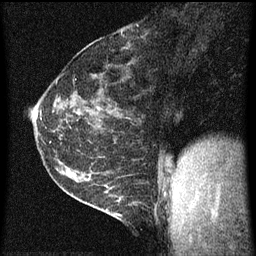
Breast MRI (dynamic contrast-enhanced), one sagittal slice. Position 25 of 60 along the scan axis. Dynamic contrast-enhanced series, image 2 of 3 at this slice position (ordered by acquisition). 1.5 T. TE 4.2 ms, TR 8 ms. 256 × 256 image matrix, field of view 180 × 180 mm. Female patient, age 35 years.
Outlined on this slice (semi-automatic segmentation, software-assisted and operator-edited):
- analysis volume of interest (the breast-tissue region the enhancement analysis was run in; not a lesion): bounding box (x1, y1, x2, y2) in pixels: (106, 182, 143, 223)
- tumour enhancement mask (voxels above the 70 % enhancement threshold inside the analysis volume of interest): (114, 198, 123, 217)